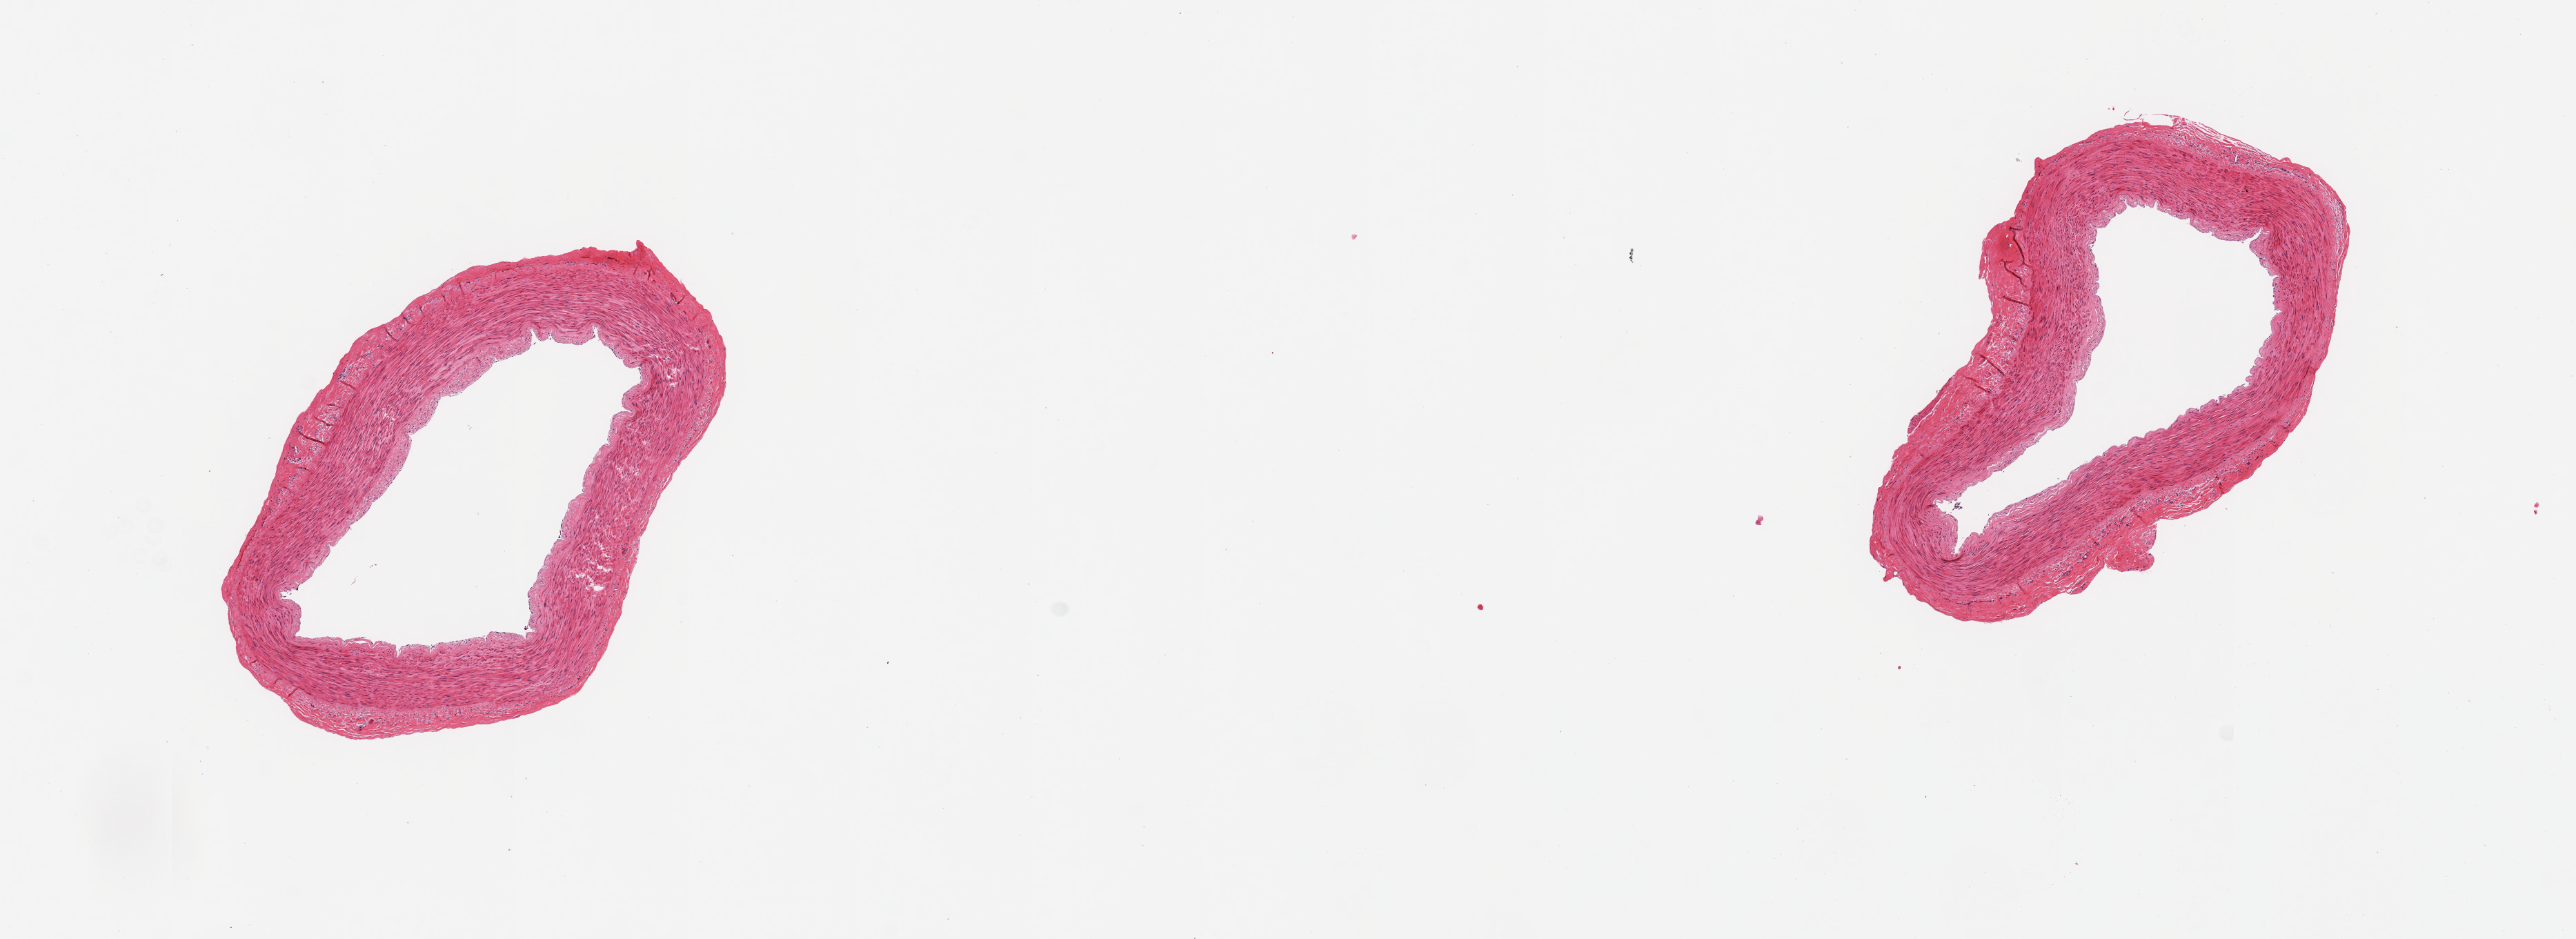
Hematoxylin and eosin (H&E) whole-slide image, whole scanned area (about 14.8 x 5.4 mm) shown as a low-resolution overview, PAXgene-fixed, paraffin-embedded tissue, target tissue: tibial artery, tissue donor sample. Donor: male.
• review note (as recorded): 2 pieces, no adherent fat or significant atherosis